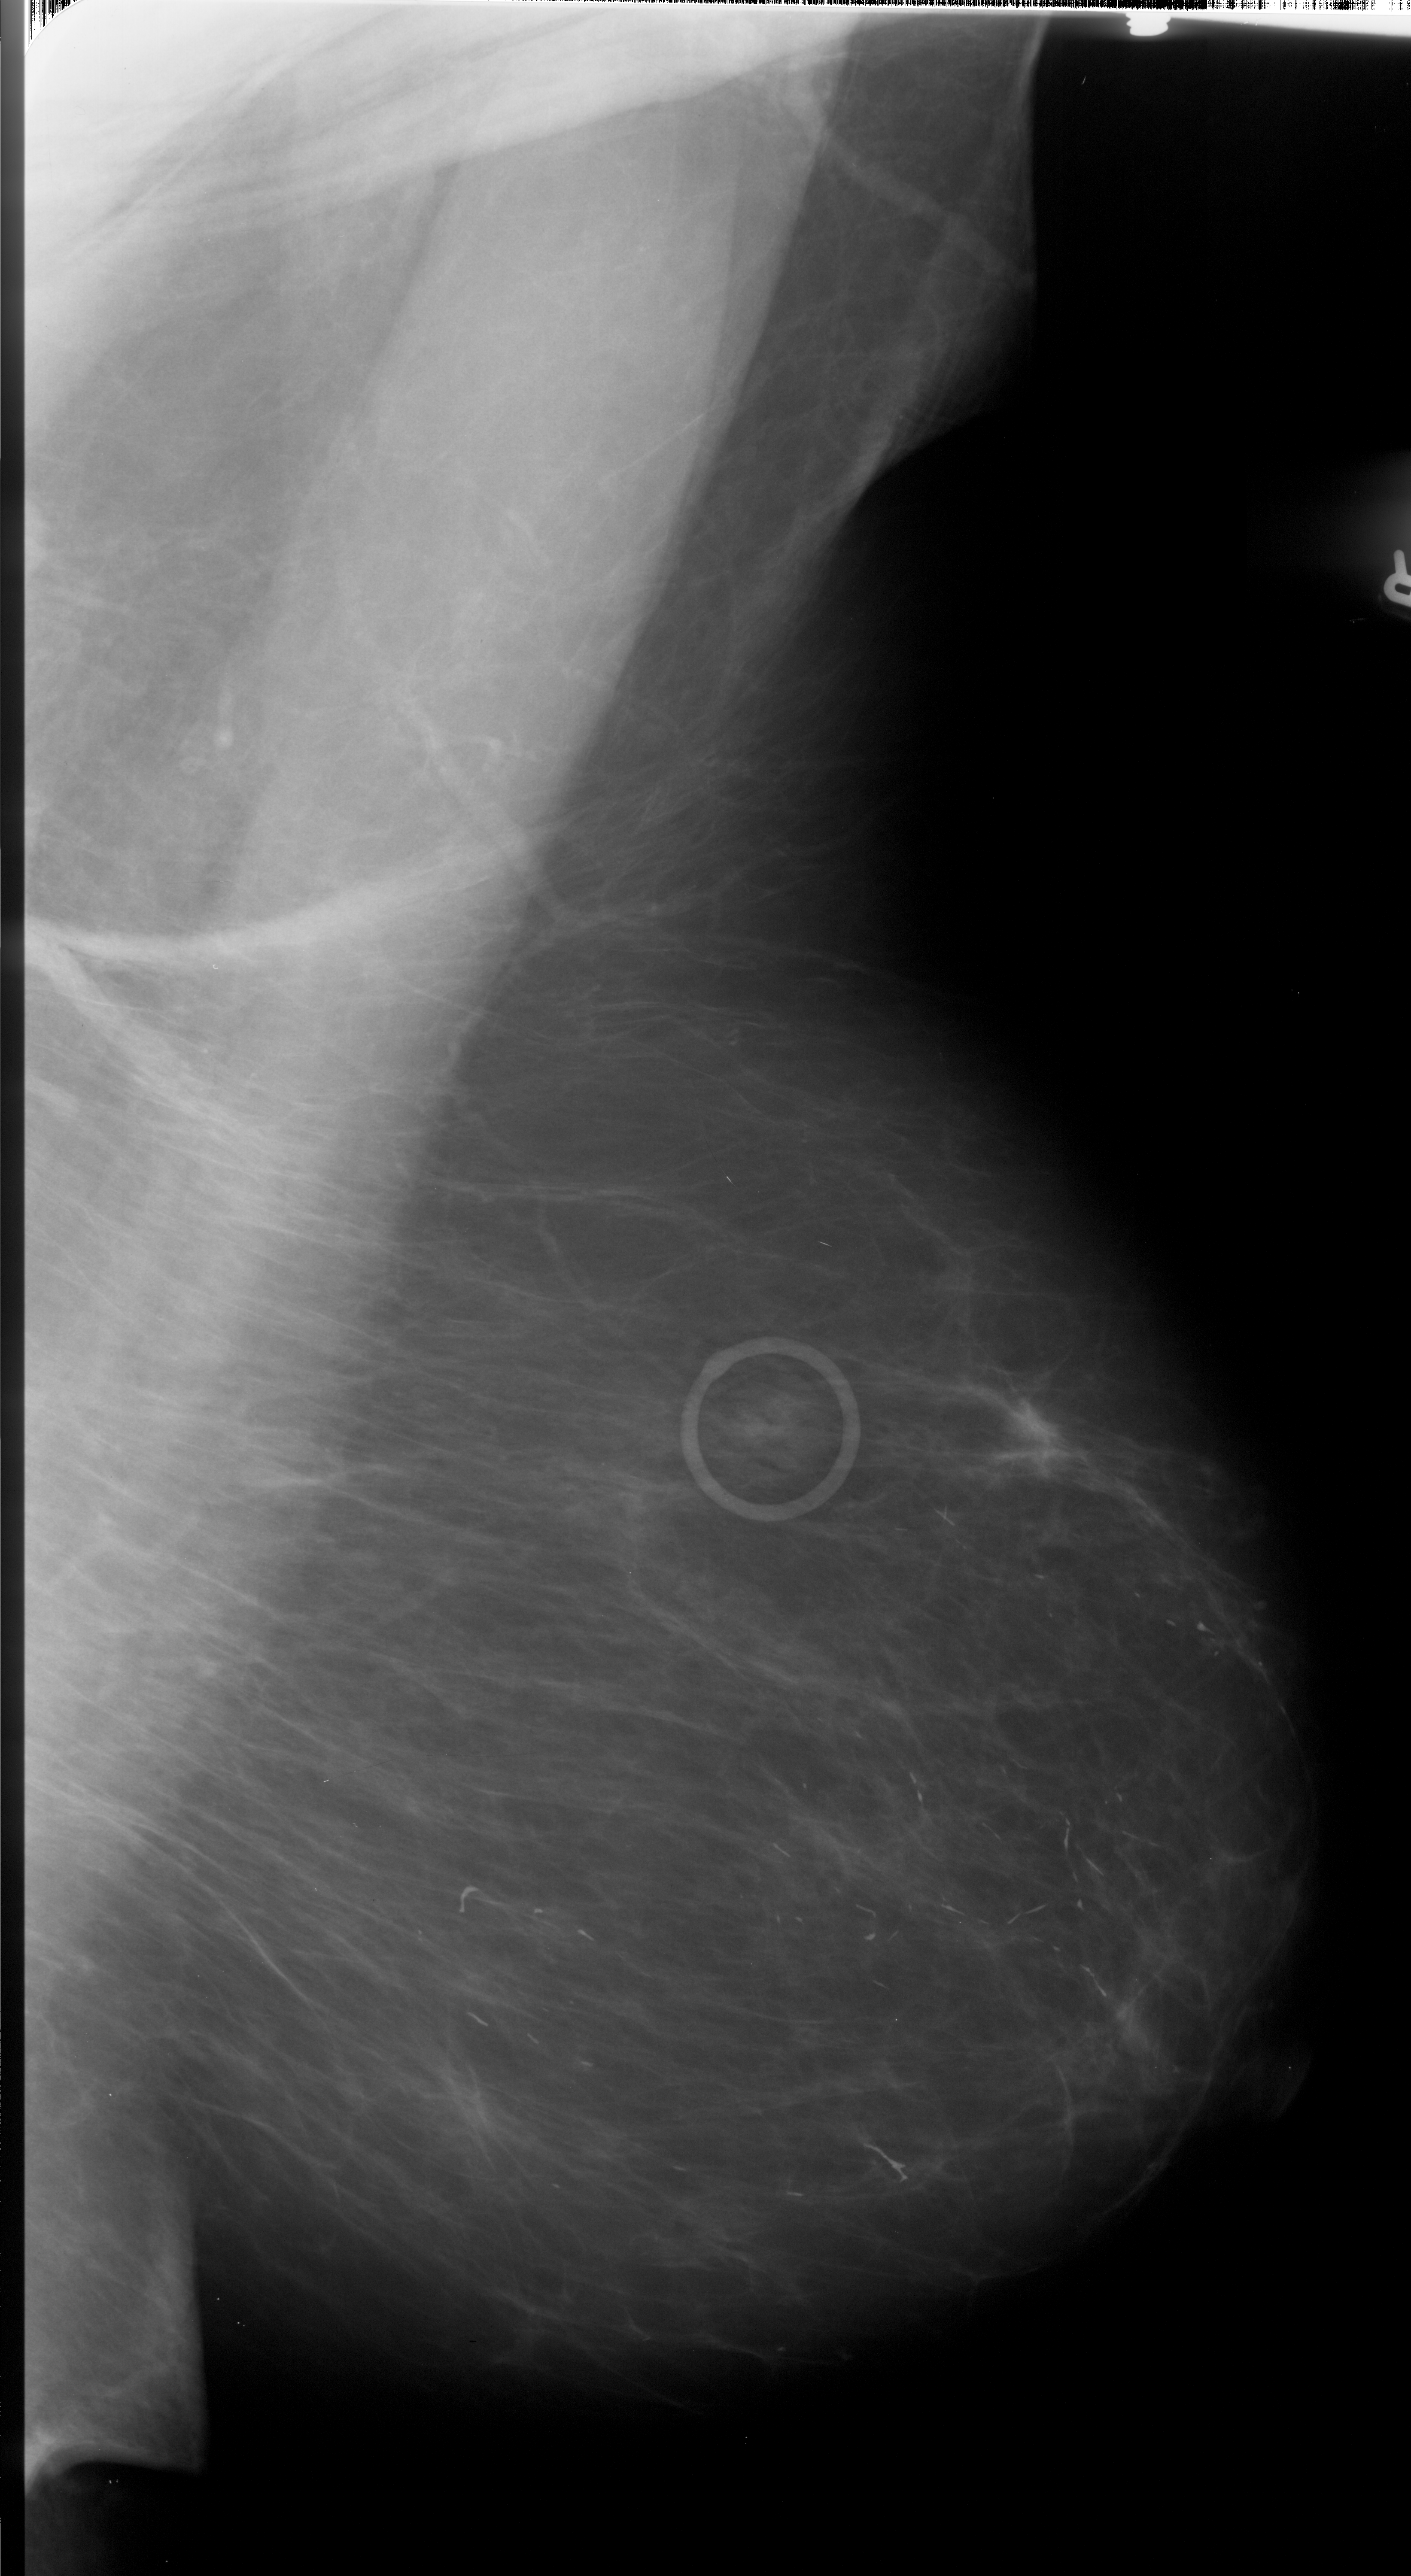
Scanned film-screen mammogram. Right breast. Mediolateral oblique (MLO) view. 1411 × 2576 image matrix.
Marked abnormalities (boxes around the expert regions of interest):
- mass, shape irregular, margins spiculated; BI-RADS assessment category 5; pathology result (as recorded, not read from the image): malignant: bounding box [x1, y1, x2, y2] px = [989, 1395, 1087, 1484]